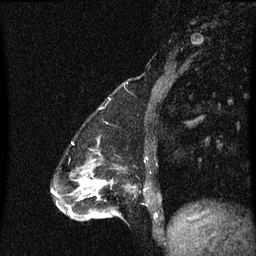
Breast MRI (dynamic contrast-enhanced), one sagittal slice; slice 20 of 60 in the series (ordered by position); dynamic contrast-enhanced series, image 2 of 3 at this slice position (ordered by acquisition); 1.5 T; TE 4.2 ms, TR 8.4 ms; 2 mm slice thickness; 256 × 256 image matrix, field of view 200 × 200 mm. Female patient, age 47 years.
Structures marked on this image (semi-automatic segmentation, software-assisted and operator-edited):
- analysis volume of interest (the breast-tissue region the enhancement analysis was run in; not a lesion): bounding box <100,180,151,219> (left, top, right, bottom; pixels)
- tumour enhancement mask (voxels above the 70 % enhancement threshold inside the analysis volume of interest): <100,180,107,187>